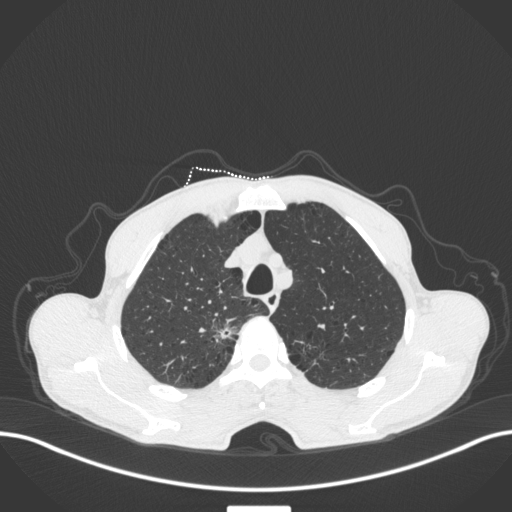
Chest CT, one axial slice; slice 346 of 445 in the series (ordered by position); 120 kVp; lung window (W 1500 / L -600 HU); 1 mm slice thickness; 512 × 512 image matrix, field of view 400 × 400 mm. Patient: male, 70 years. Case-level facts recorded for this patient, not image findings: clinical TNM (as recorded): T1a N0 M0.
Outlined on this slice (bounding box drawn by a radiologist):
- lung tumour (recorded histology: adenocarcinoma): bounding box (x1, y1, x2, y2) in pixels: (210, 319, 241, 349)